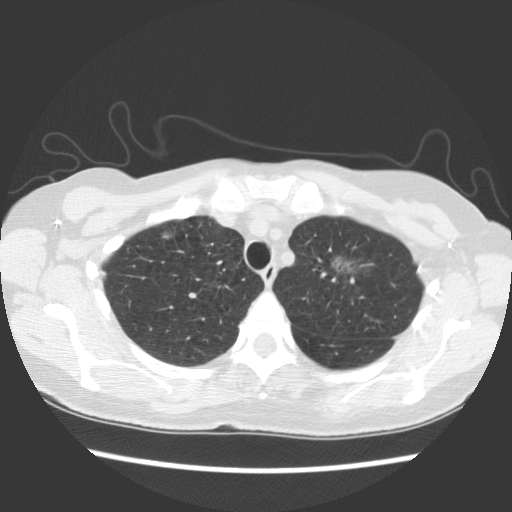
Axial slice from a low-dose chest CT screening exam; baseline screening round; lung window (W 1500 / L -600 HU). Female, age 65 years at enrolment. Former smoker at enrolment.
Expert-annotated lung lesion, box from (x=312, y=240) to (x=380, y=298) px. Reader record for this screening exam (exam-level; its link to the box is not recorded): non-calcified nodule or mass ≥4 mm, left upper lobe, 11 × 10 mm, poorly defined margins, ground glass attenuation.